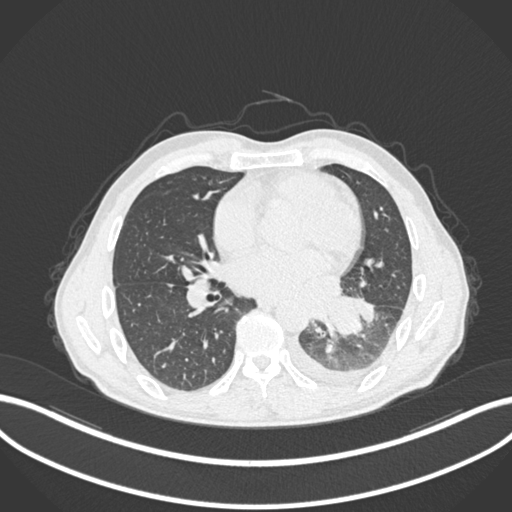
Chest CT, one axial slice. Slice 108 of 222 in the series (ordered by position). Reconstruction kernel B30f. 120 kVp. Lung window (W 1500 / L -600 HU). 1 mm slice thickness. 512 × 512 image matrix. Male patient, age 47 years. Case-level facts recorded for this patient, not image findings: clinical TNM (as recorded): T3 N1 M1c; histopathological grade: G3.
Structures marked on this image (rectangle marked by the reading radiologist):
- lung tumour (recorded histology: small cell carcinoma): bounding box (x1, y1, x2, y2) in pixels: (321, 293, 363, 338)